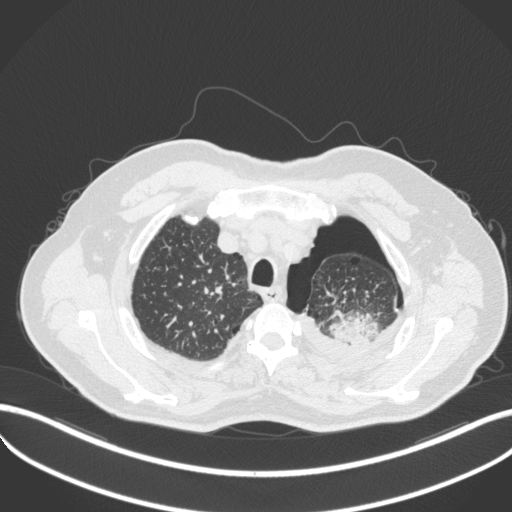
Chest CT, one axial slice; slice 416 of 466 in the series (ordered by position); reconstruction kernel B31f; 120 kVp; lung window (W 1500 / L -600 HU); 1 mm slice thickness; 512 × 512 image matrix, field of view 400 × 400 mm. Male patient, age 76 years. Case-level facts recorded for this patient, not image findings: clinical TNM (as recorded): T3 N0 M1b.
Annotated regions visible in this slice (rectangle marked by the reading radiologist):
- lung tumour (recorded histology: adenocarcinoma): bounding box (x1, y1, x2, y2) in pixels: (323, 308, 382, 349)